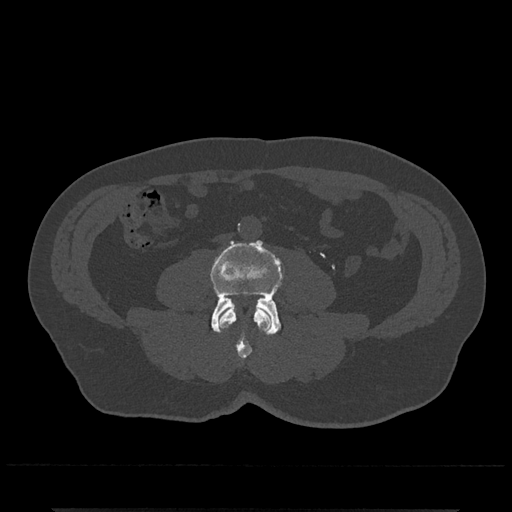
CT including the spine, one axial slice. Reconstruction kernel Br40s/3. 120 kVp. Bone window (W 1800 / L 400 HU). 0.5 mm slice thickness. 512 × 512 image matrix, field of view 393 × 393 mm. Patient: male, 67 years. Case-level facts recorded for this patient, not image findings: primary cancer: prostate.
Outlined on this slice (semi-automatically segmented with operator editing):
- L3 vertebra: box from (x=219, y=307) to (x=272, y=360) px
- L4 vertebra: (x=210, y=241)–(x=284, y=335)